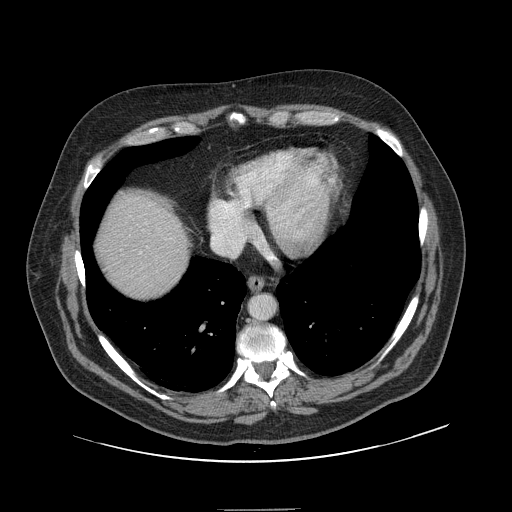
Contrast-enhanced abdominal CT, one axial slice; 120 kVp; soft-tissue window (W 400 / L 40 HU); 2.5 mm slice thickness; 512 × 512 image matrix, field of view 451 × 451 mm. Male patient, age 61 years. Case-level facts recorded for this patient, not image findings: diagnosis: colorectal cancer liver metastases, imaged before liver resection; multiple liver metastases: yes; largest metastasis: 2.6 cm.
Structures marked on this image (manually delineated by an expert):
- liver: bounding box (x1, y1, x2, y2) in pixels: (97, 193, 188, 298)
- planned liver remnant (the part of the liver to remain after resection): (97, 193, 188, 298)